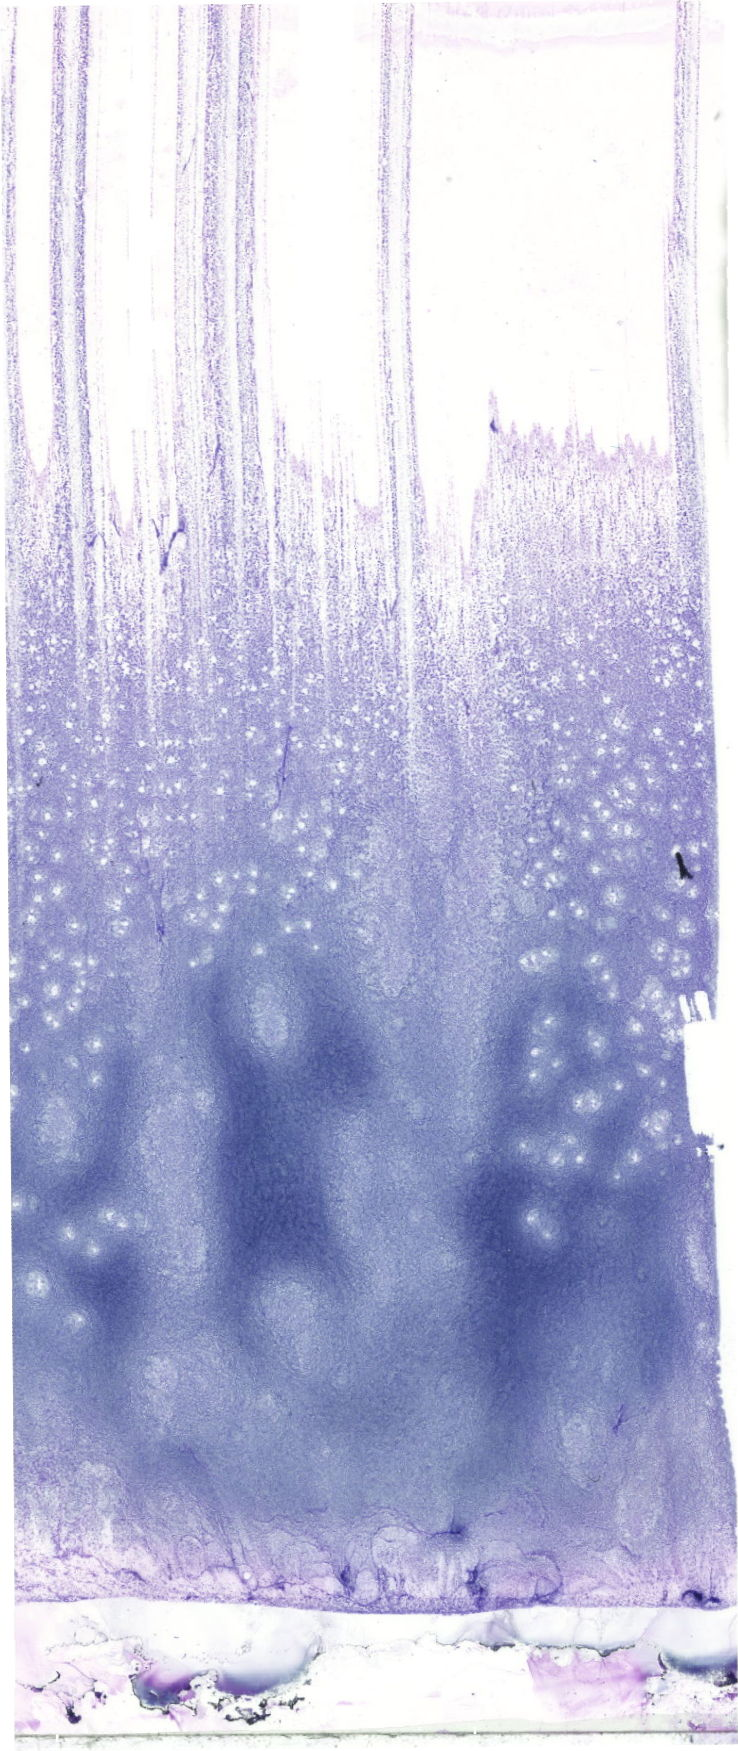
Whole-slide image of a May-Grünwald–Giemsa-stained bone marrow aspirate smear — low-resolution overview of the scanned area, about 20.9 x 49.6 mm. Female patient.
Diagnosis: B Acute Lymphoblastic Leukemia.